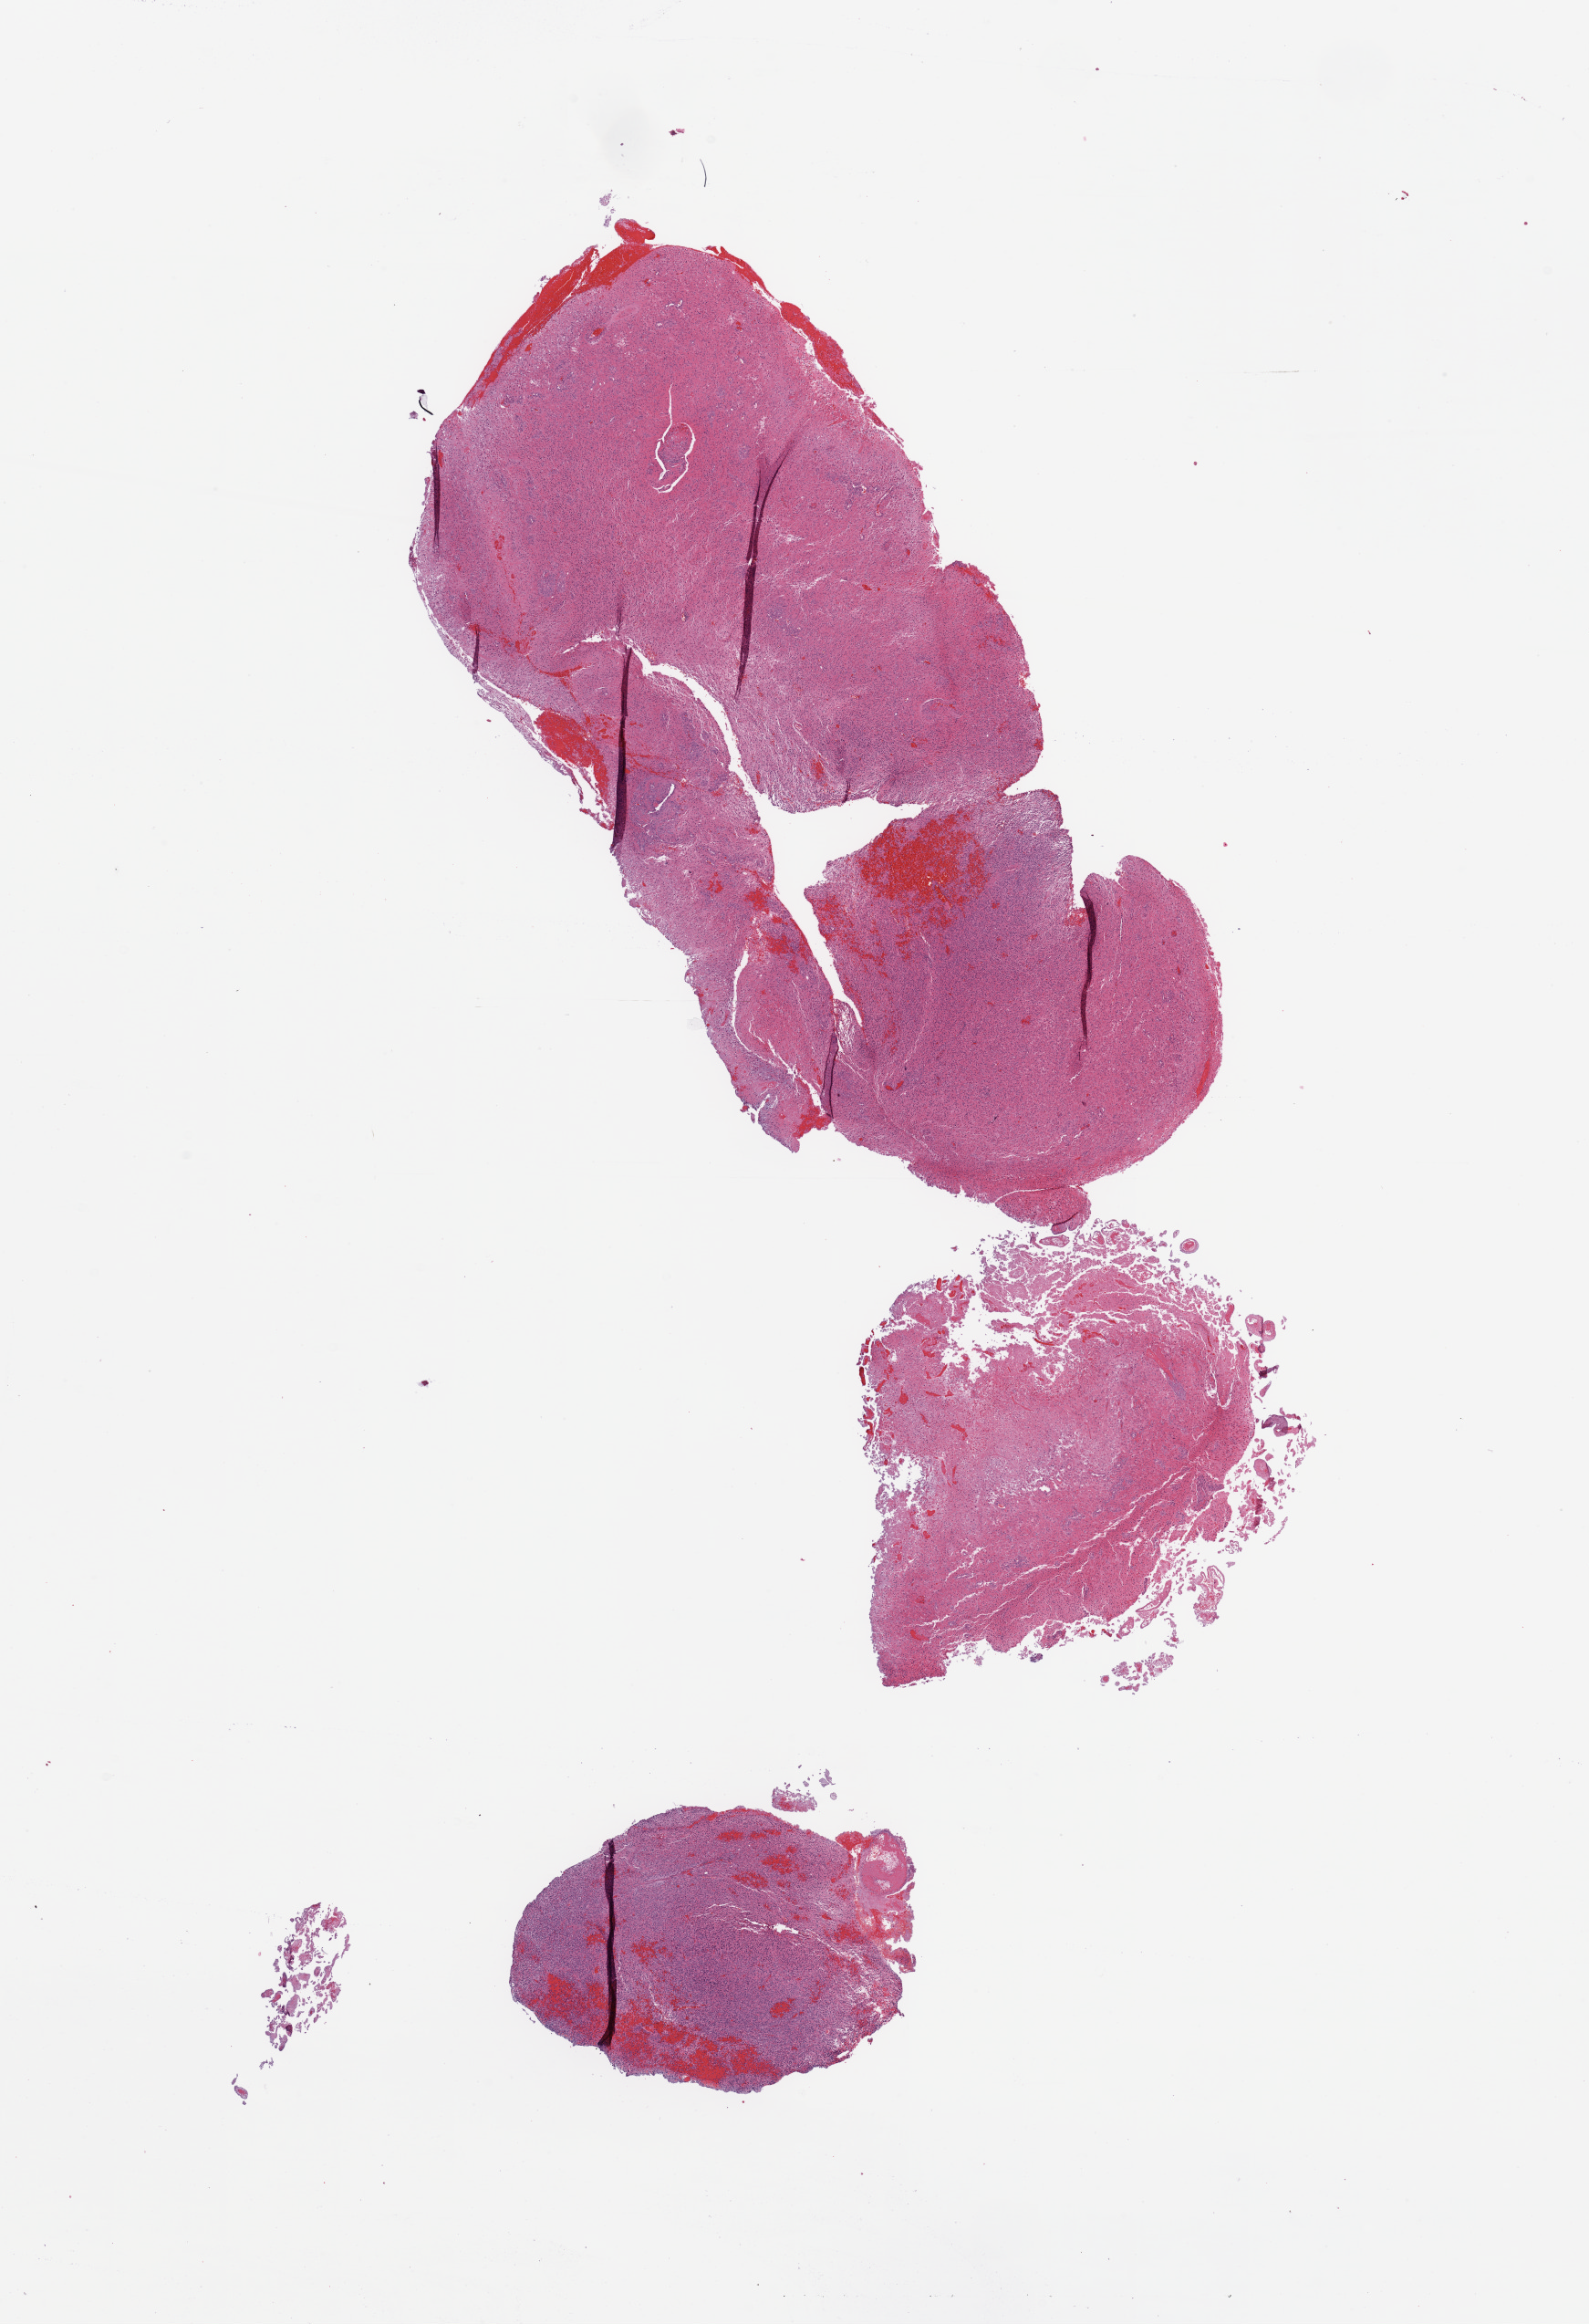
H&E whole-slide image — shown as a low-resolution overview of the whole scanned area (about 13.8 x 20.2 mm, acquisition: 20x scan); tumour tissue sample, sampled site: frontal lobe. 54-year-old male patient. Slide review estimates, as recorded: tumour nuclei 75%, necrosis 10%.
Primary tumour site (as recorded): frontal lobe. Histologic diagnosis: Glioblastoma.